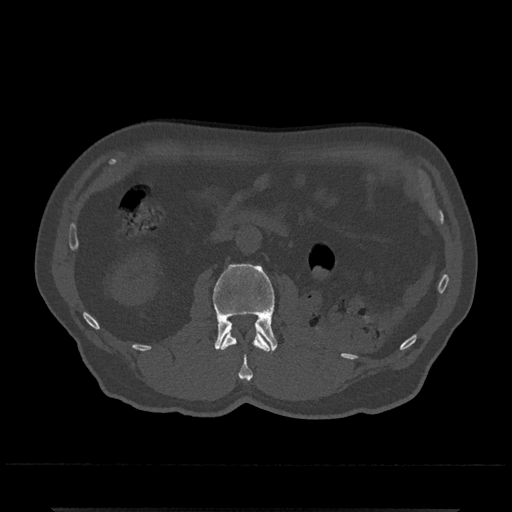
CT including the spine, one axial slice. Slice 314 of 797 in the series (ordered by position). Bone window (W 1800 / L 400 HU). 512 × 512 image matrix, field of view 393 × 393 mm. Male patient, age 67 years. From the clinical record (not read from this slice): primary cancer: prostate.
Structures marked on this image (semi-automatic segmentation, software-assisted and operator-edited):
- L1 vertebra: bounding box (x1, y1, x2, y2) in pixels: (220, 330, 270, 380)
- L2 vertebra: (213, 264, 278, 353)